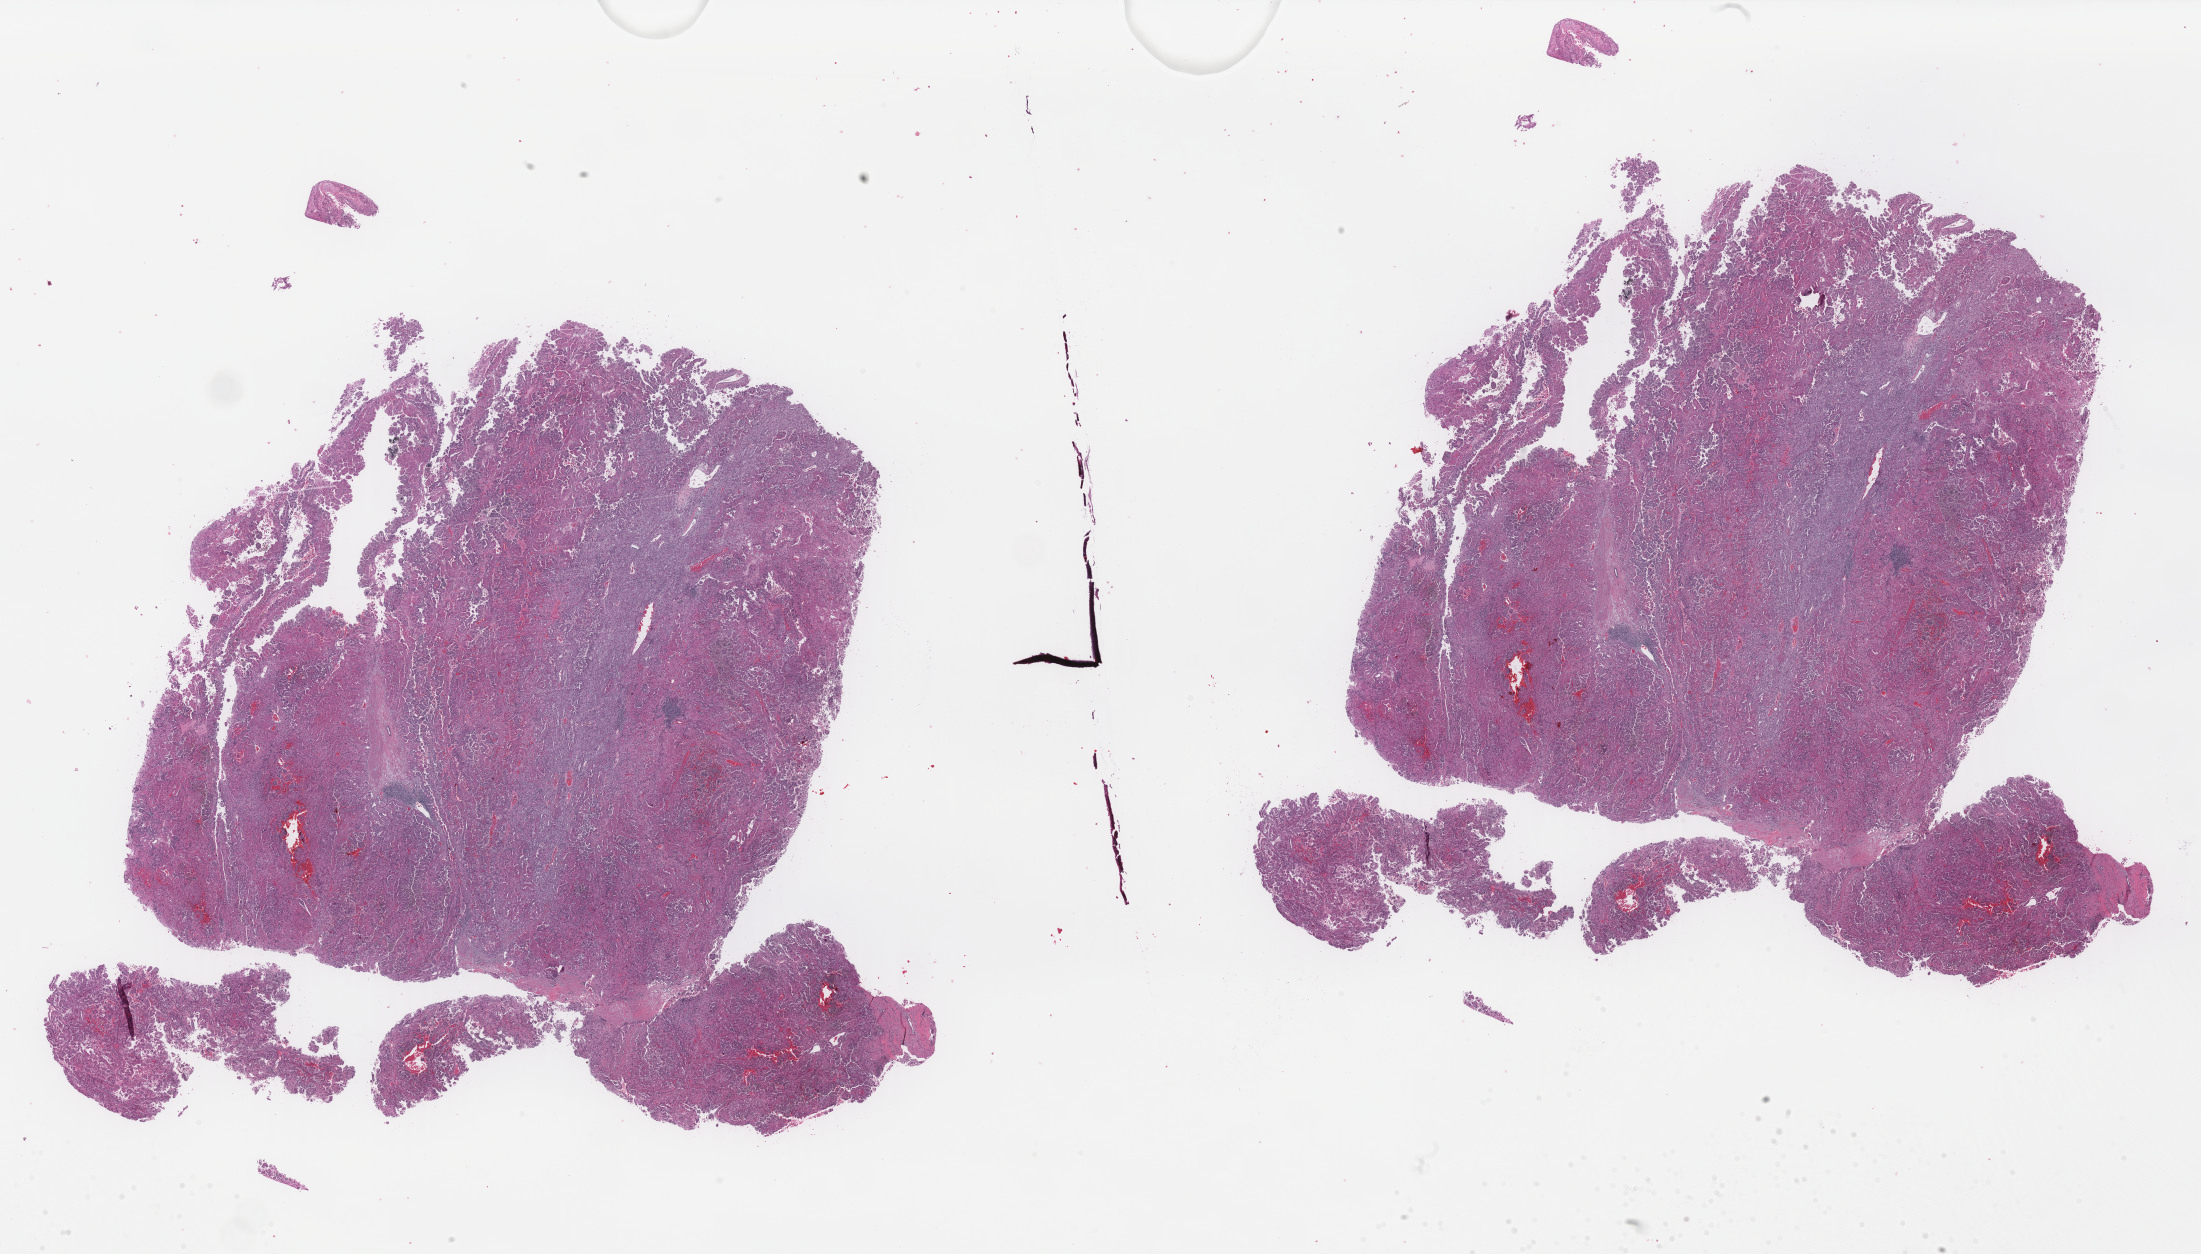
Hematoxylin and eosin (H&E) stained whole-slide image — whole scanned area (about 34.8 x 19.8 mm, from a 40x scan) shown as a low-resolution overview. Formalin-fixed paraffin-embedded (FFPE) diagnostic section. Kidney, primary tumour sample. Male, age 71 years at initial diagnosis.
- laterality: left
- diagnosis: Papillary adenocarcinoma, NOS
- AJCC pathologic stage: III (7th edition)